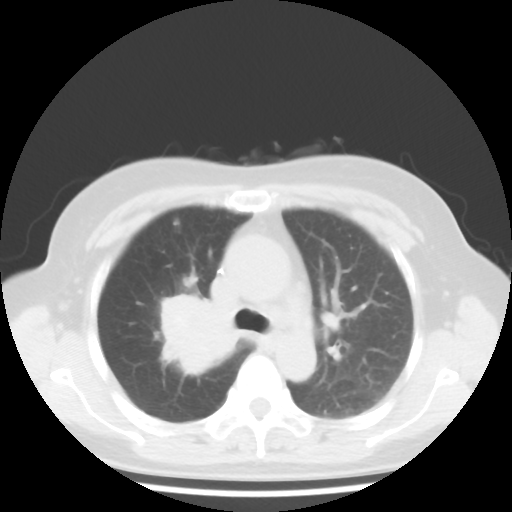
Chest CT, one axial slice. Position 28 of 43 along the scan axis. Reconstruction kernel STANDARD. 100 kVp. Lung window (W 1500 / L -600 HU). 5 mm slice thickness. 512 × 512 image matrix, field of view 316 × 316 mm. Female patient, age 62 years. From the clinical record (not read from this slice): clinical TNM (as recorded): T3 N0 M0; histopathological grade: G3.
Structures marked on this image (bounding box drawn by a radiologist):
- lung tumour (recorded histology: small cell carcinoma): bounding box [x1, y1, x2, y2] px = [152, 280, 244, 380]